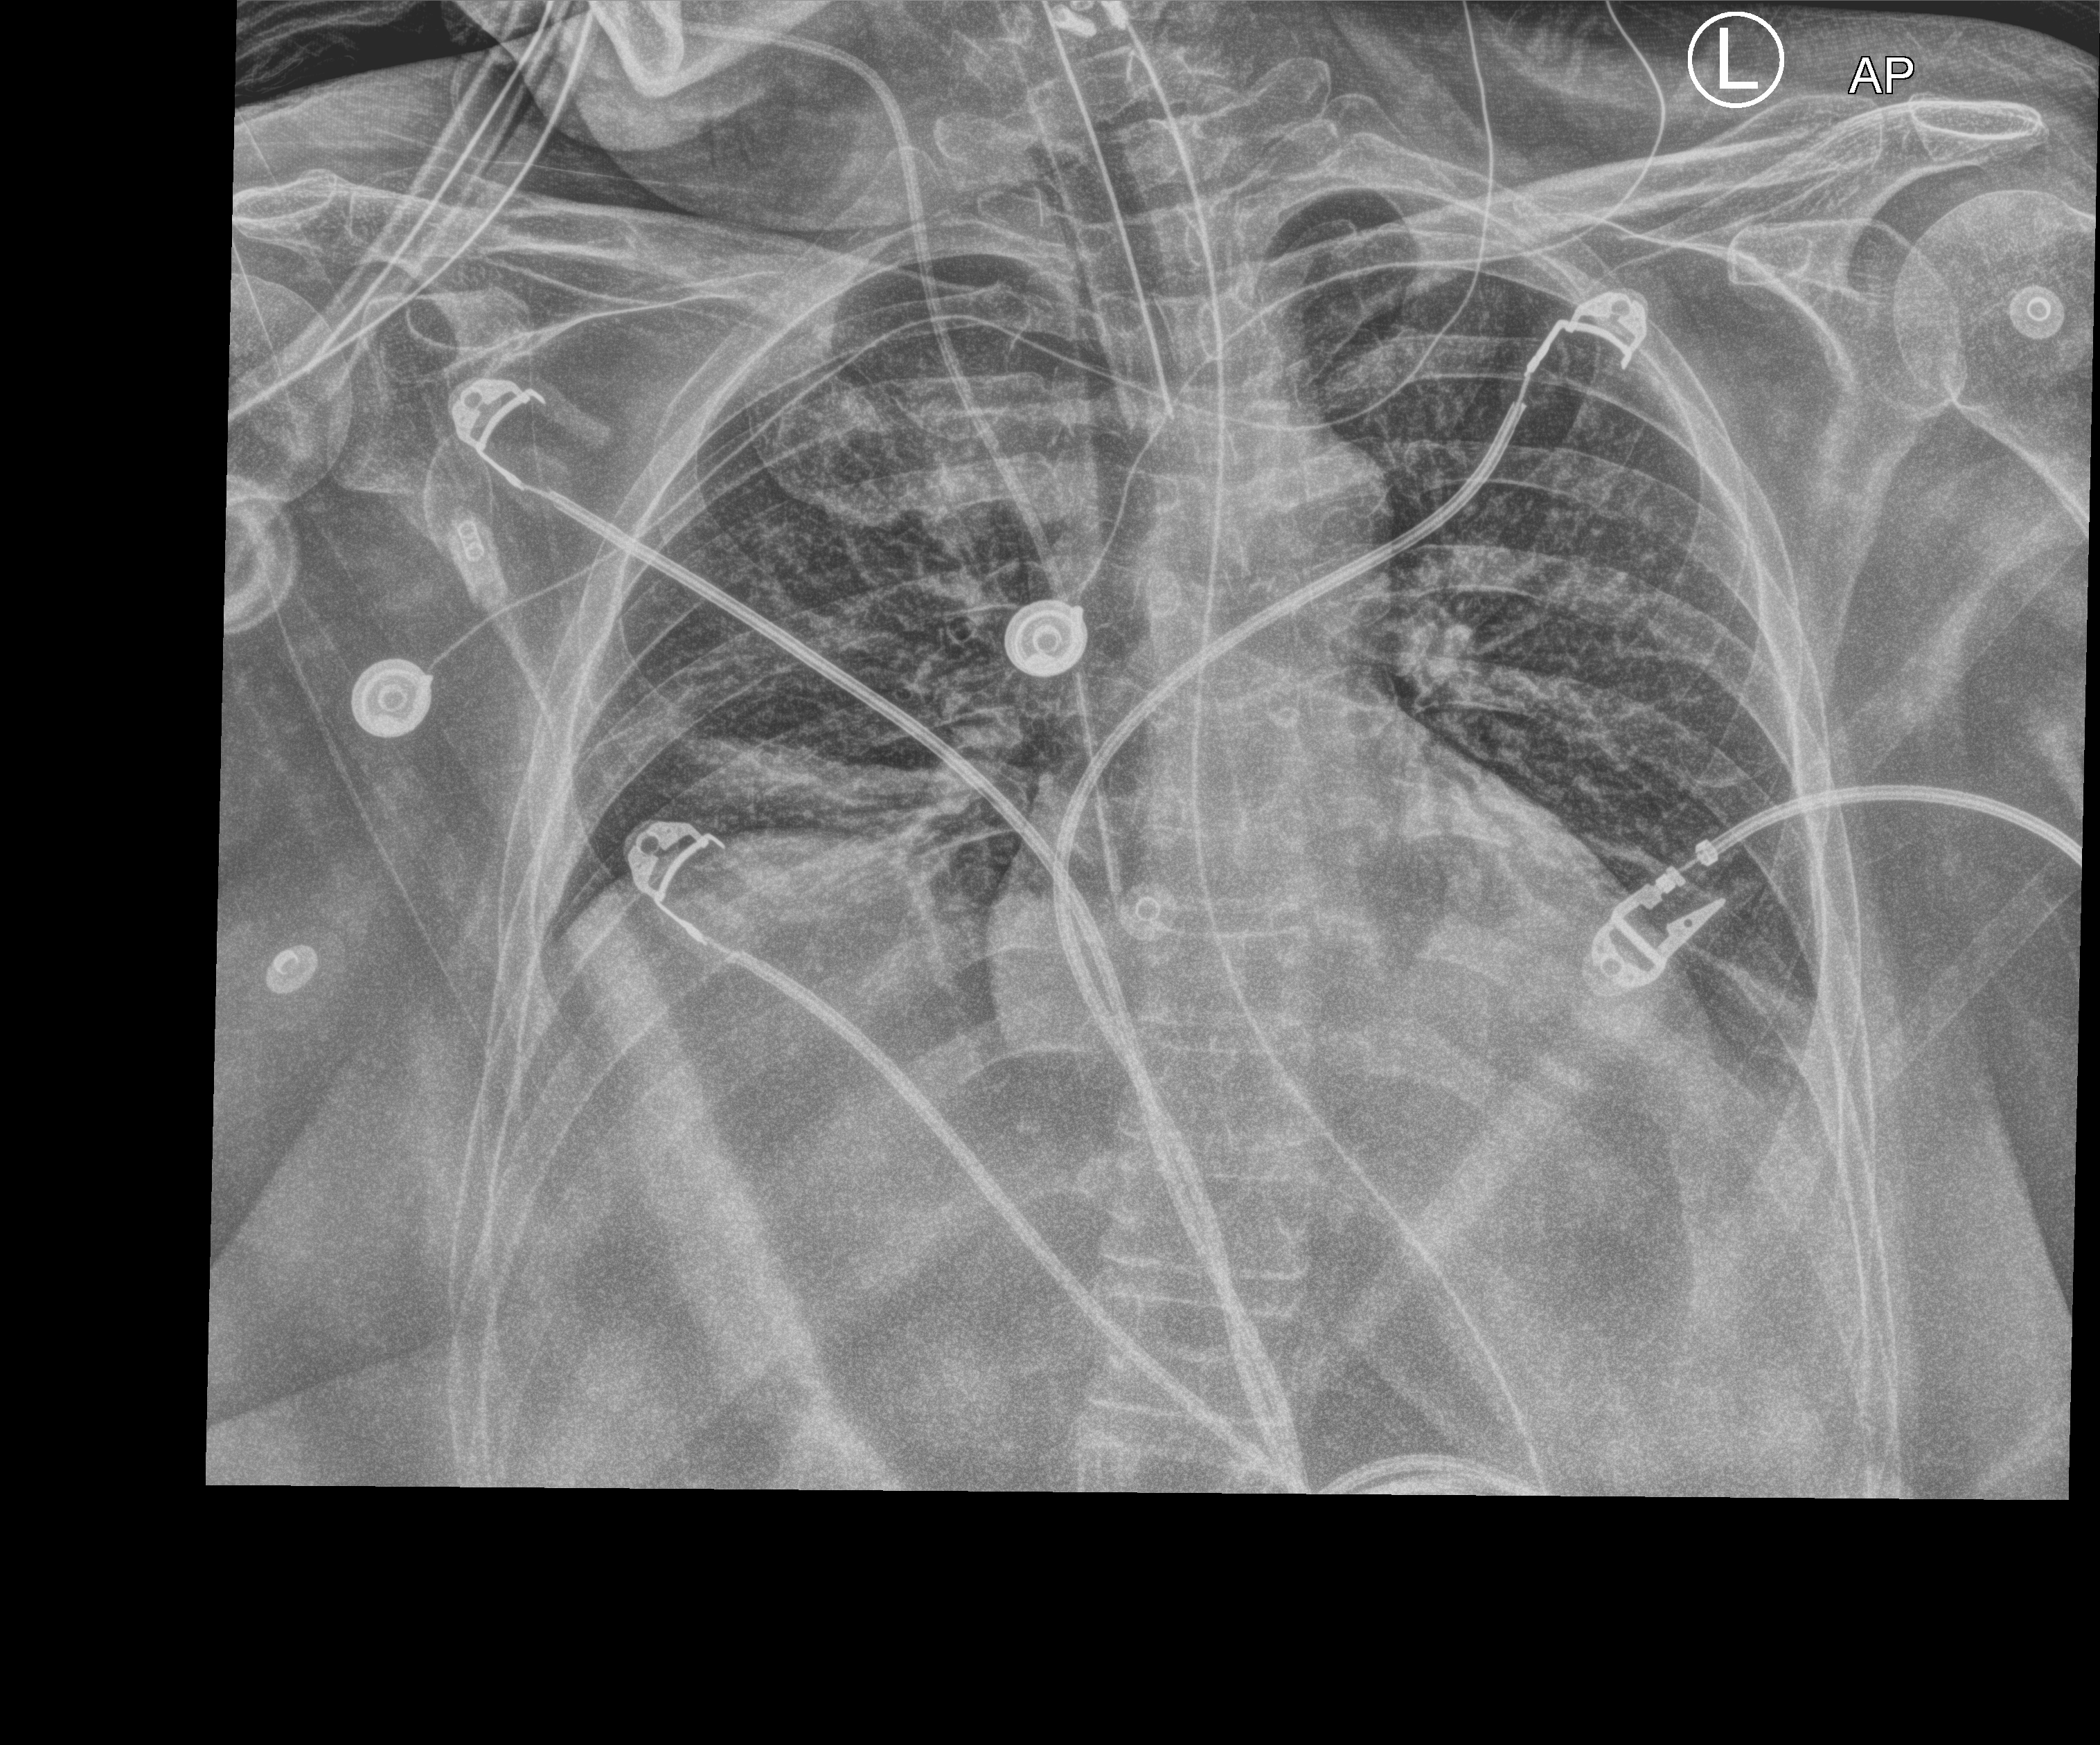
Portable chest radiograph; anteroposterior (AP) projection. Female patient hospitalised with COVID-19, age 18–59 years.
From the hospital-stay record, not from the radiograph (when in the stay this image was taken is not recorded): mechanically ventilated during this hospital stay: no.